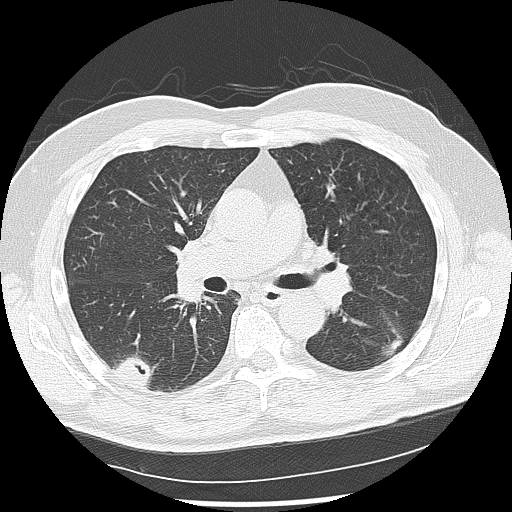
Low-dose screening chest CT, one axial slice; slice 76 of 142 in the series (ordered by position); 120 kVp; lung window (W 1500 / L -600 HU); 512 × 512 image matrix.
Structures marked on this image (manually delineated by an expert):
- lesion 1 (nodule, lower lobe of left lung): bounding box (x1, y1, x2, y2) in pixels: (381, 338, 404, 357)
- lesion 2 (nodule, lower lobe of right lung): (113, 355, 156, 387)